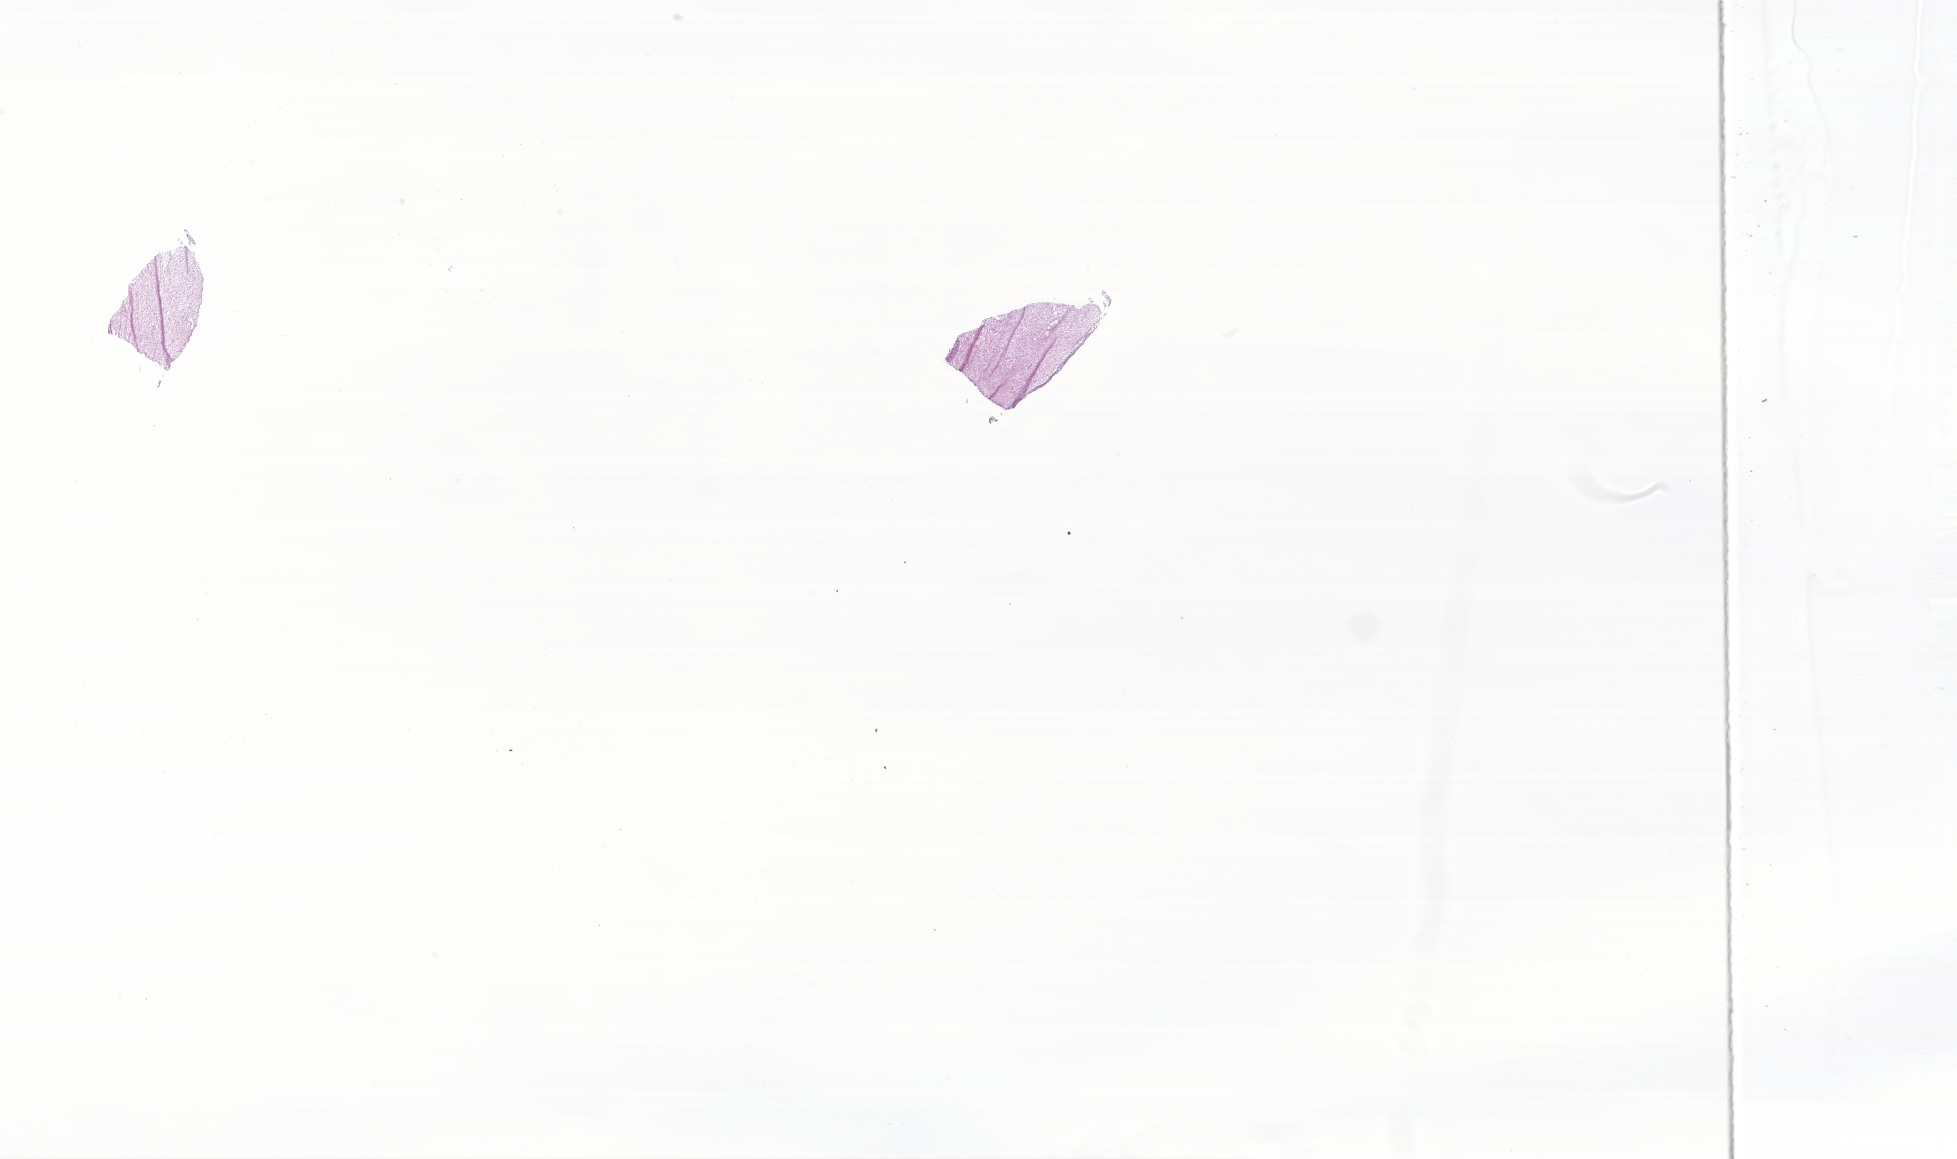
Haematoxylin and eosin whole-slide image of tumor tissue from the brain stem, a low-resolution overview of the entire scanned area, about 33.0 x 19.5 mm, cryosection (OCT / tissue freezing medium). Male patient, age 78 months (6 years 6 months).
Diagnosis: Pilocytic astrocytoma.